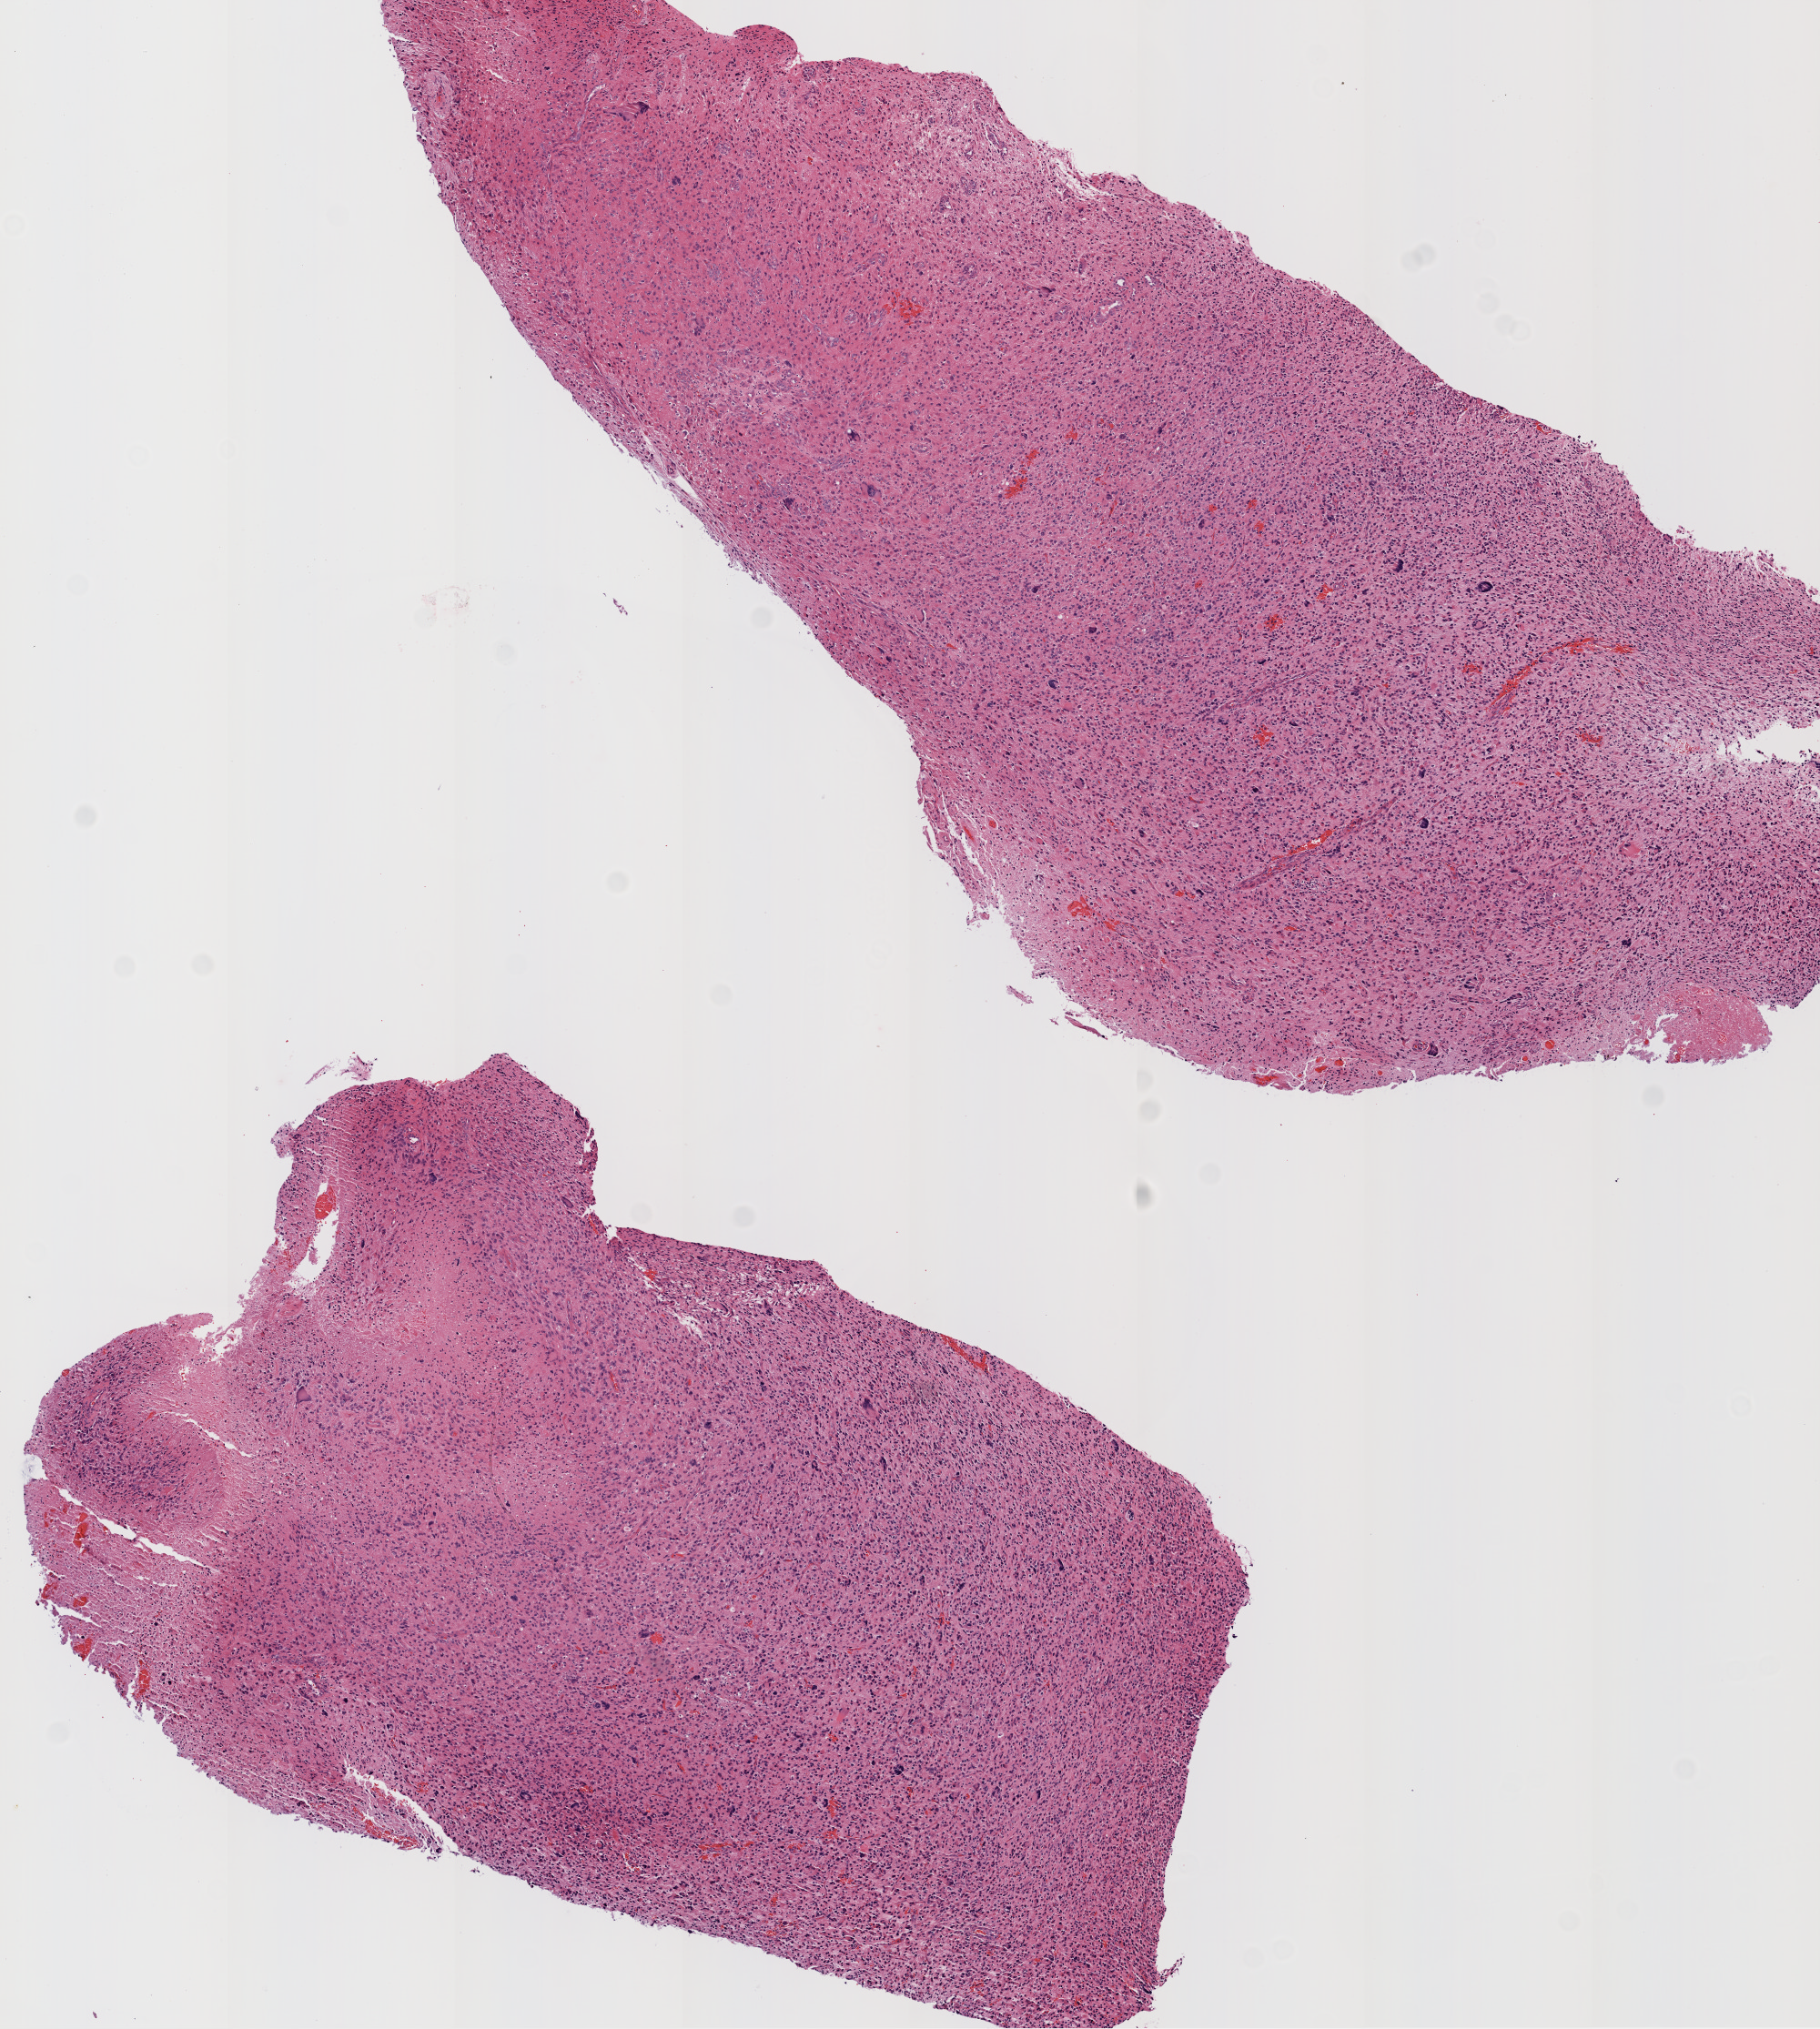
H&E whole-slide image — a low-resolution overview of the entire scanned area, about 8.0 x 8.9 mm (acquisition: 20x scan); formalin-fixed paraffin-embedded (FFPE) diagnostic section; brain, primary tumour sample. Patient: male, age at initial diagnosis 69 years.
* histologic diagnosis: Glioblastoma